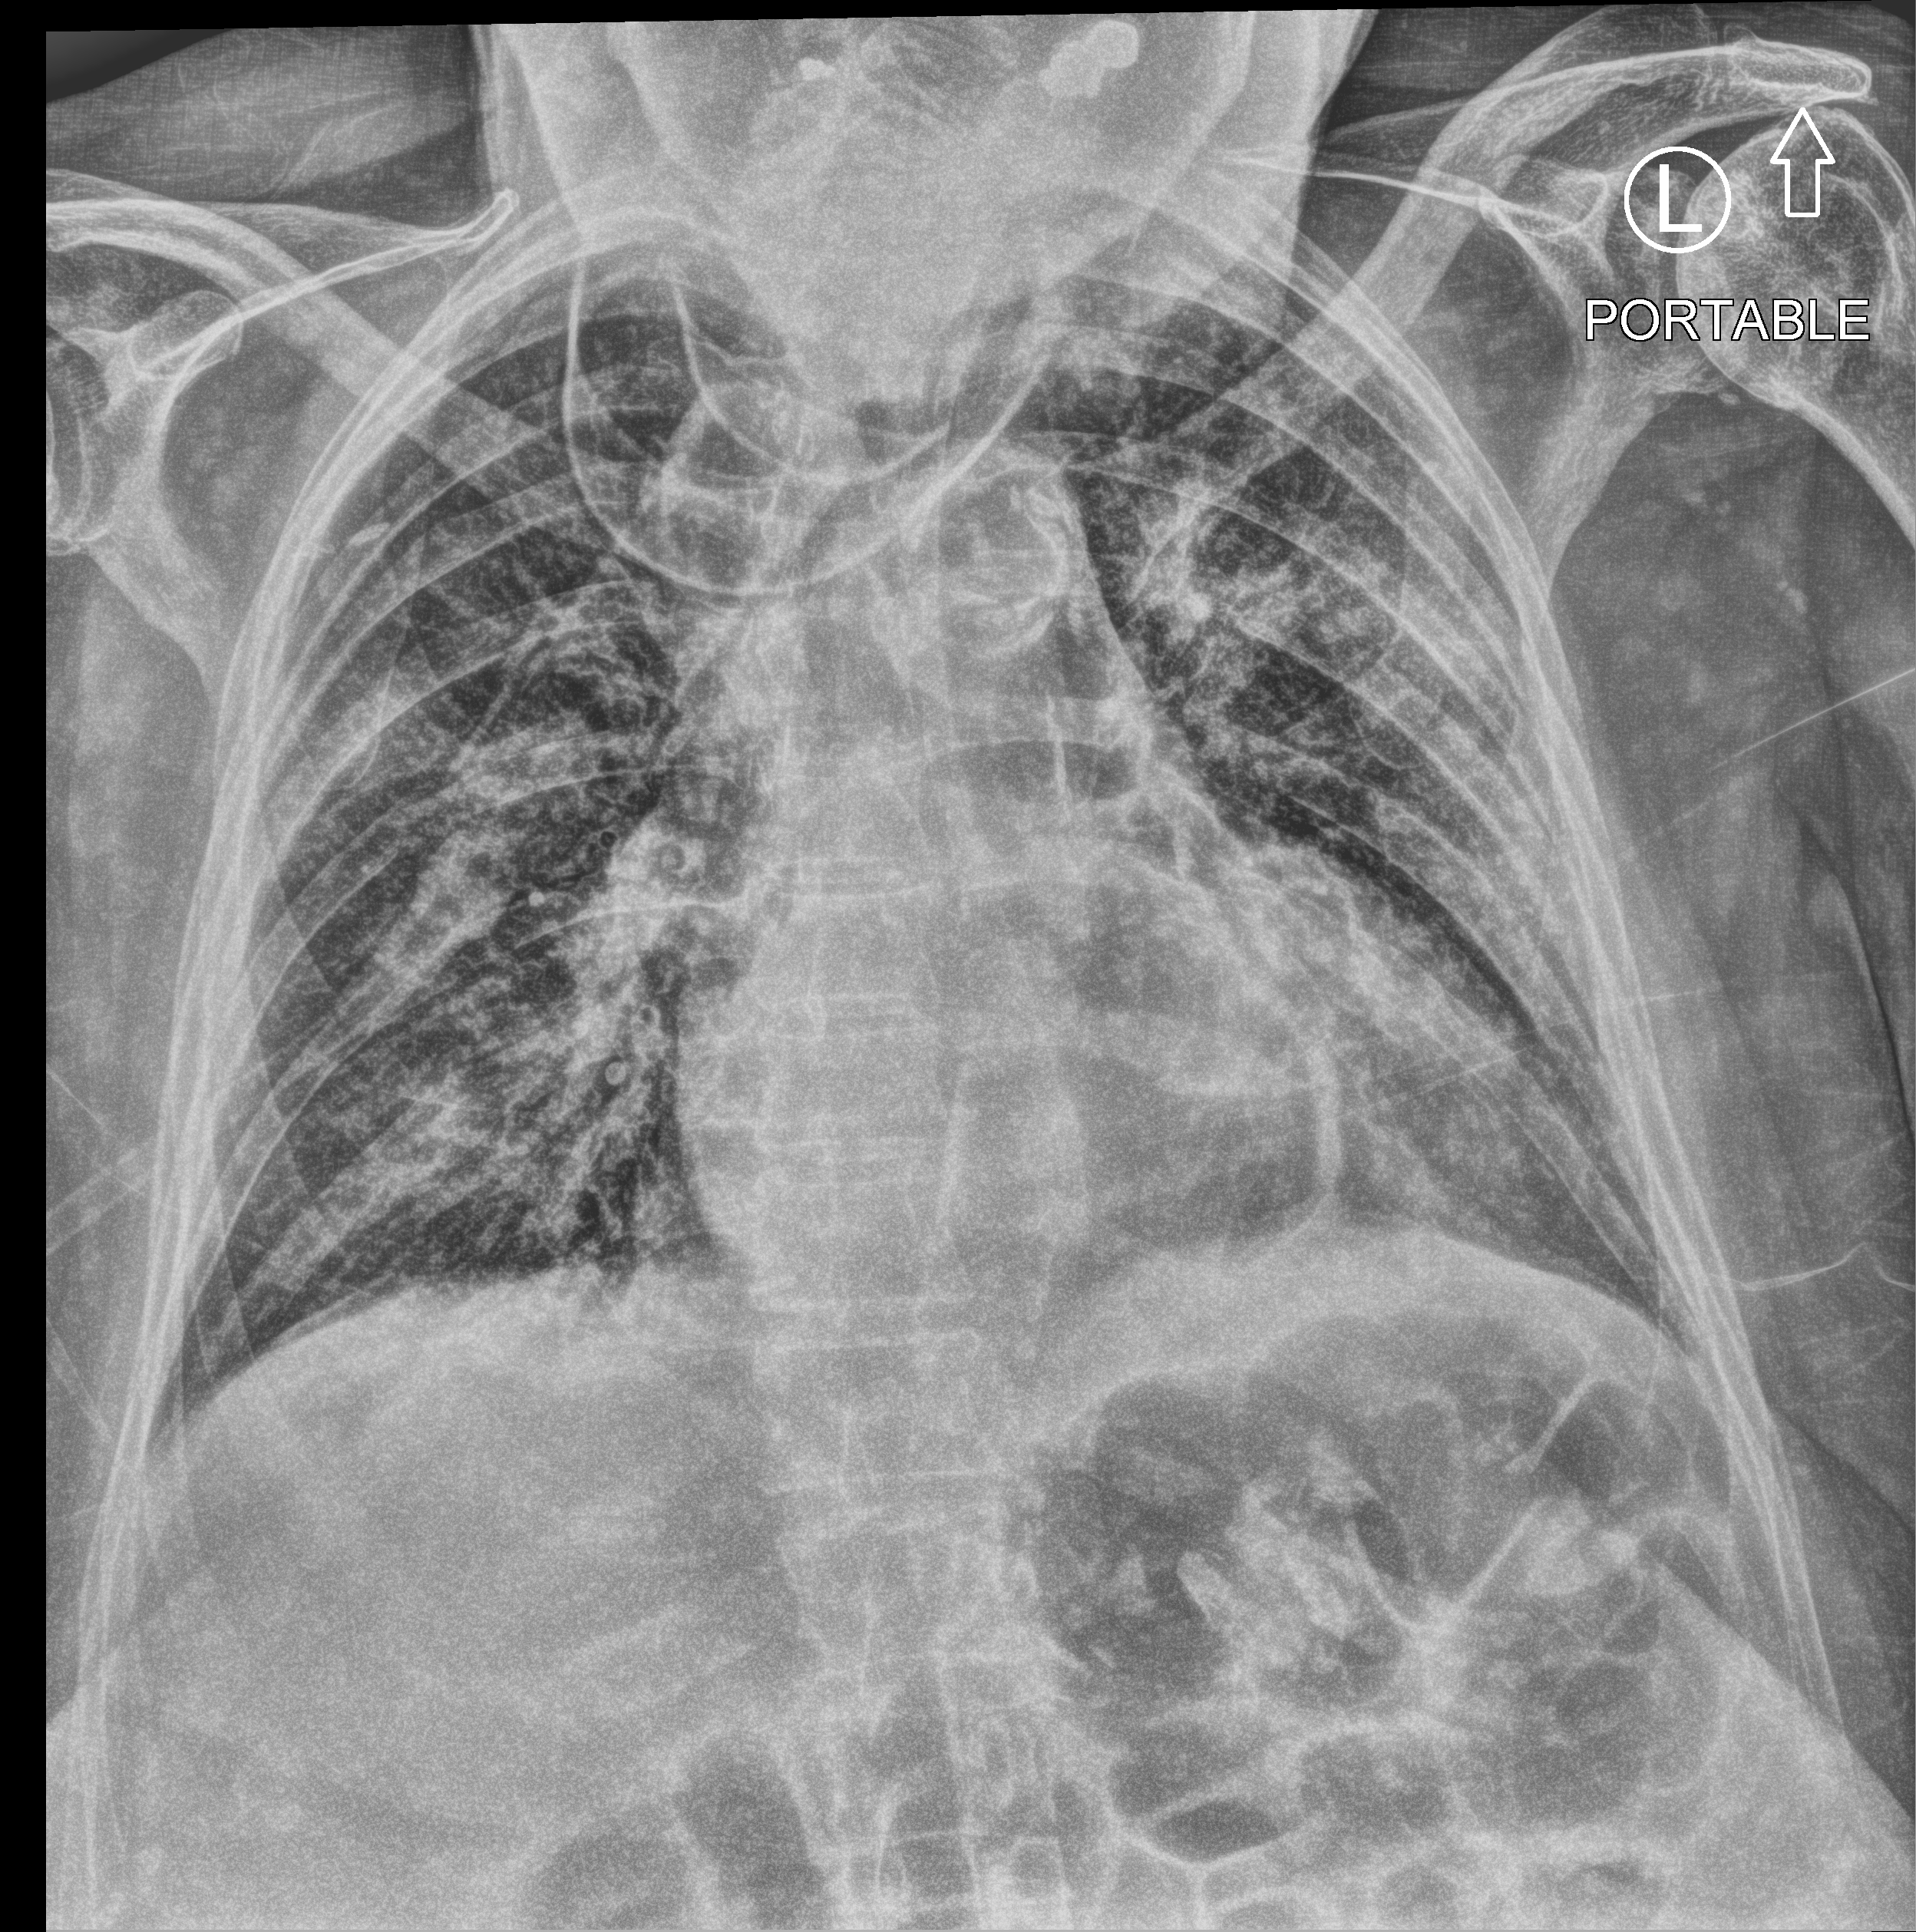
Bedside chest radiograph (computed radiography); anteroposterior (AP) projection. Patient hospitalised with COVID-19; female, aged 75–90 years.
Admission-level facts for this patient (not findings on this image; timing relative to this image not recorded): admitted to intensive care during this hospital stay: no; length of hospital stay: 13 days; mechanically ventilated during this hospital stay: no.